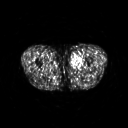
FDG PET of an extremity soft-tissue mass (from a PET/CT study), one axial slice. Slice 248 of 311 in the series (ordered by position). 3.27 mm slice thickness. 128 × 128 image matrix, field of view 500 × 500 mm. Male patient, age 29 years. Case-level facts recorded for this patient, not image findings: histological type: mixoid liposarcoma; grade: low; site of the primary tumour: left thigh.
Outlined on this slice (expert contour drawn on MRI and transferred to this co-registered scan by the dataset authors):
- gross tumour volume (mass): box from (x=70, y=53) to (x=83, y=68) px